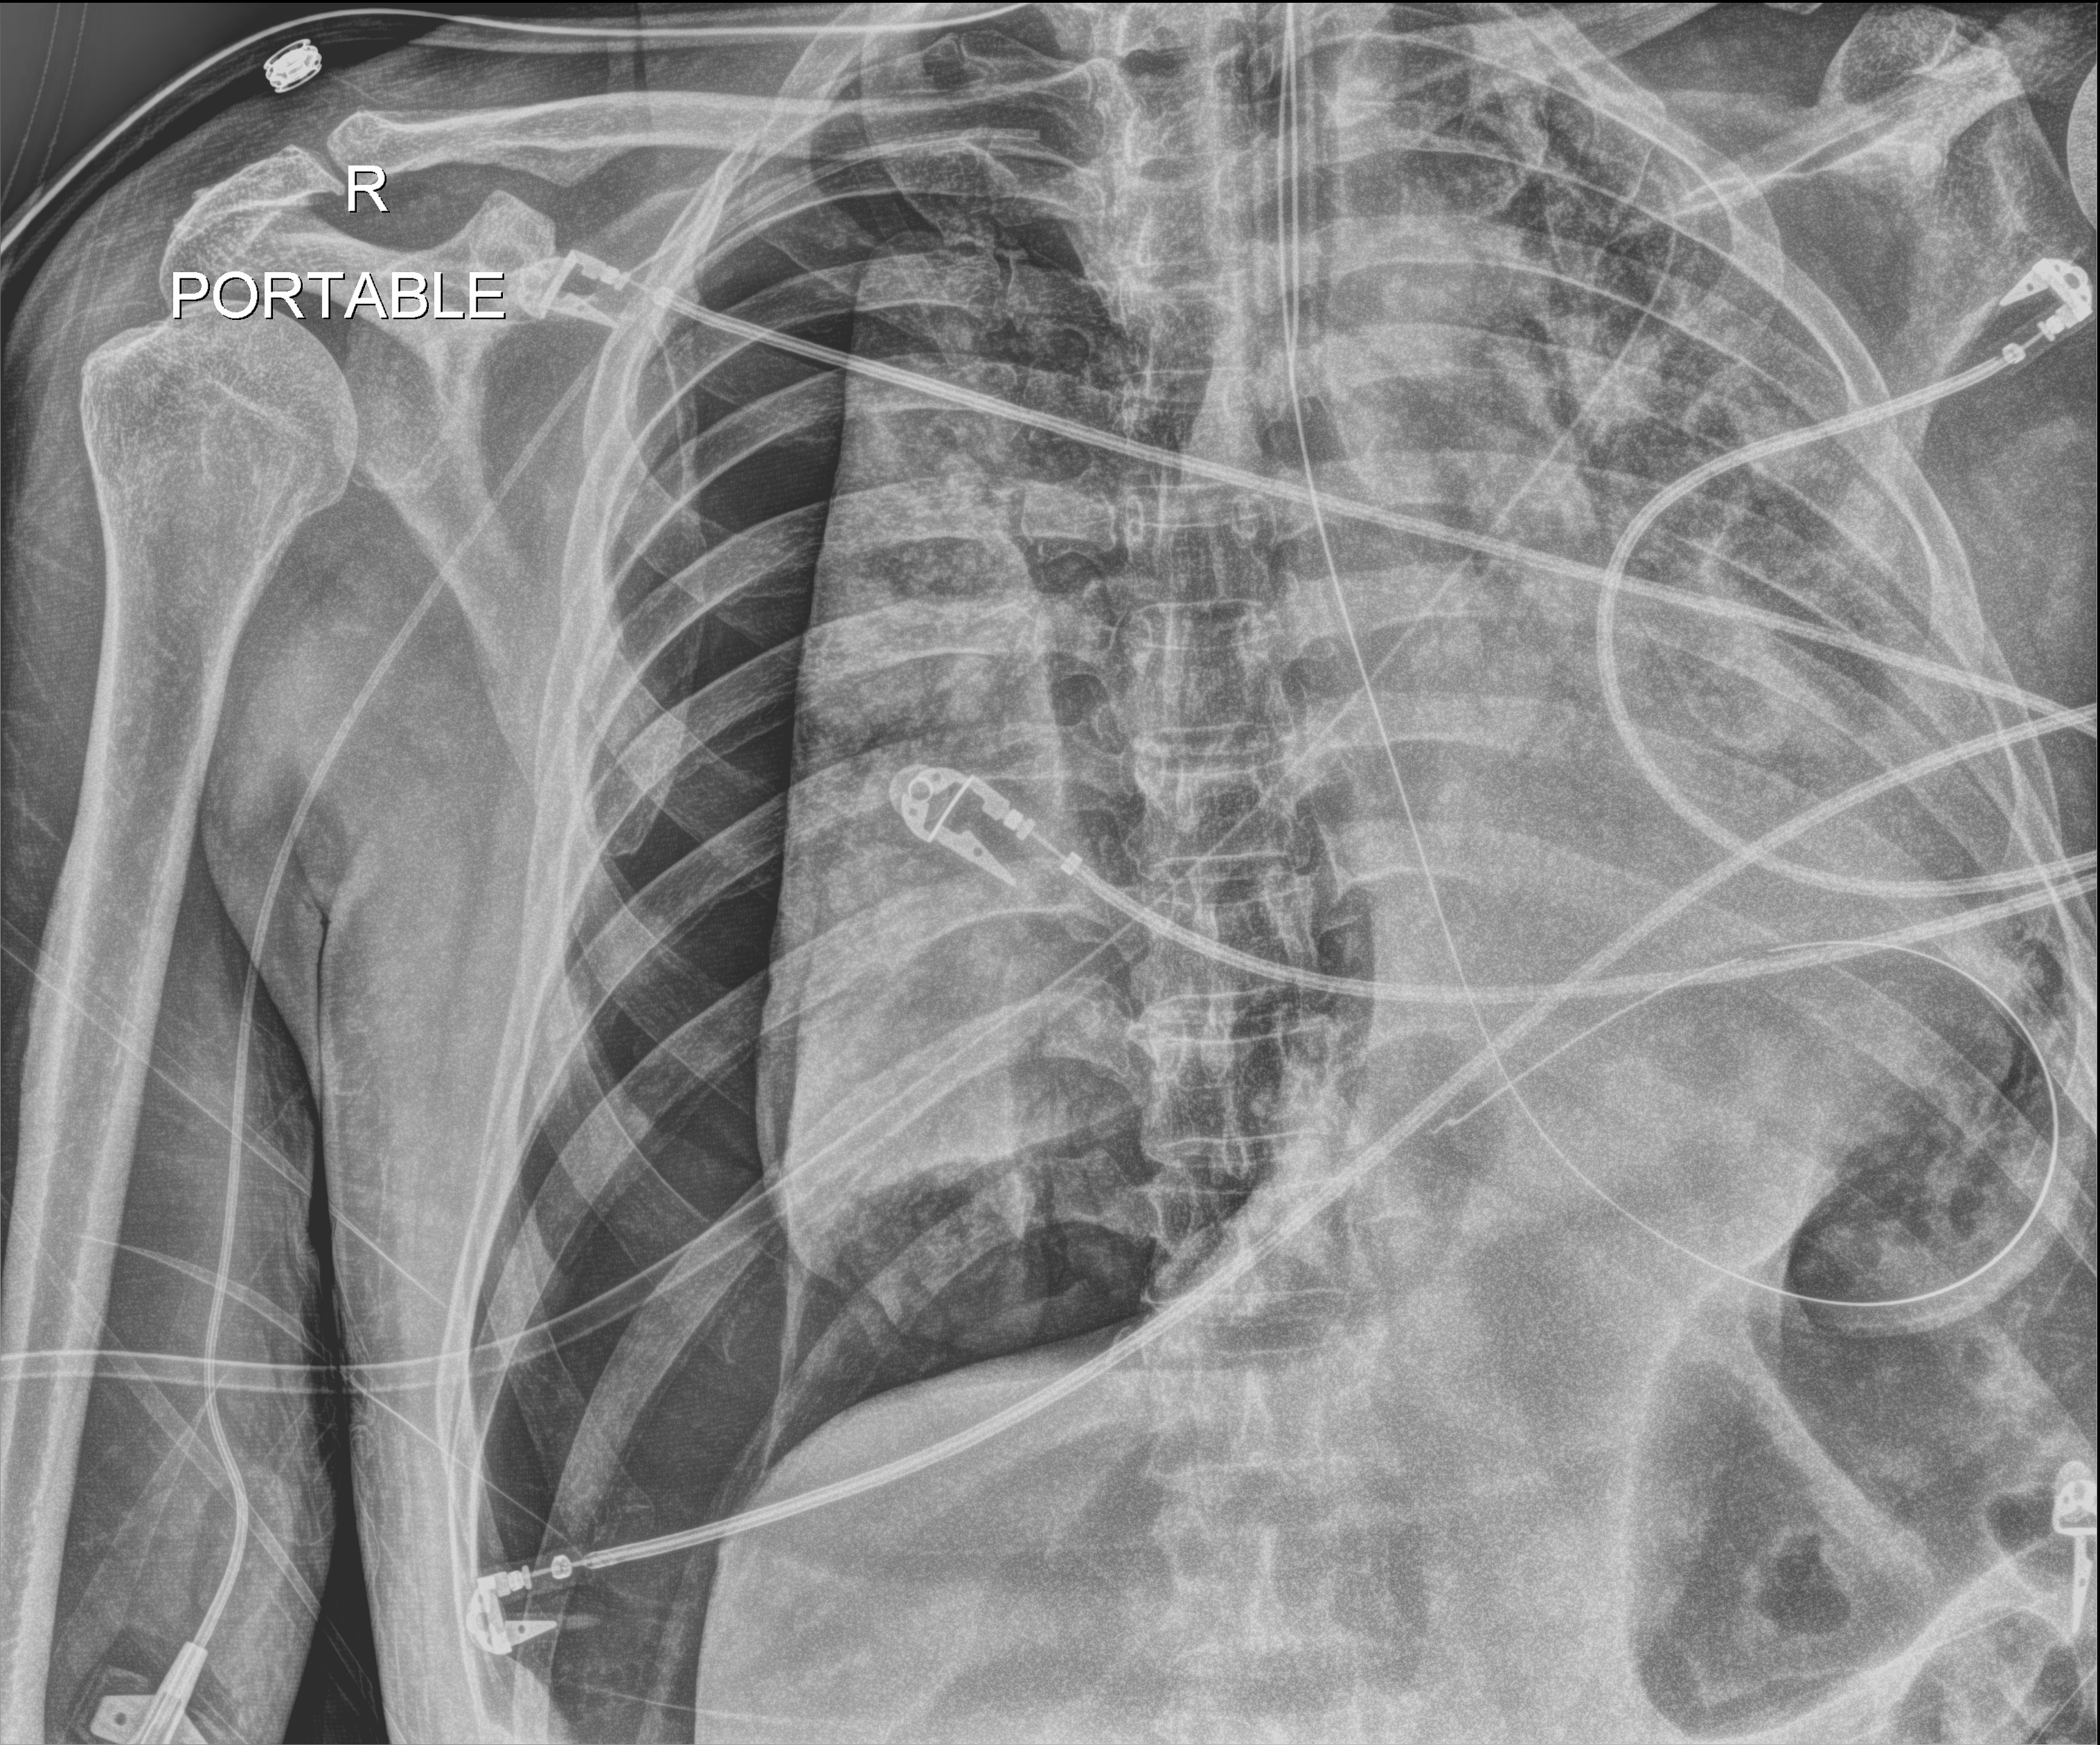
Chest X-ray, anteroposterior (AP) projection. Male patient hospitalised with COVID-19, age 60–74 years.
From the hospital-stay record, not from the radiograph (when in the stay this image was taken is not recorded): admitted to intensive care during this hospital stay: yes; chronic kidney disease (admission record): no; mechanically ventilated during this hospital stay: yes.